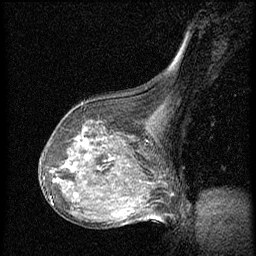
Breast MRI (dynamic contrast-enhanced), one sagittal slice; position 39 of 56 along the scan axis; dynamic contrast-enhanced series, image 2 of 3 at this slice position (ordered by acquisition); 1.5 T; TE 4.2 ms, TR 20.4 ms; 2 mm slice thickness; 256 × 256 image matrix. Female patient, age 64 years. Case-level facts recorded for this patient, not image findings: setting: breast cancer imaged before/during neoadjuvant chemotherapy; receptor status: HR-positive, HER2-negative.
Outlined on this slice (semi-automatically segmented with operator editing):
- analysis volume of interest (the breast-tissue region the enhancement analysis was run in; not a lesion): box from (x=48, y=101) to (x=142, y=186) px
- tumour enhancement mask (voxels above the 70 % enhancement threshold inside the analysis volume of interest): (x=78, y=138)–(x=87, y=145)